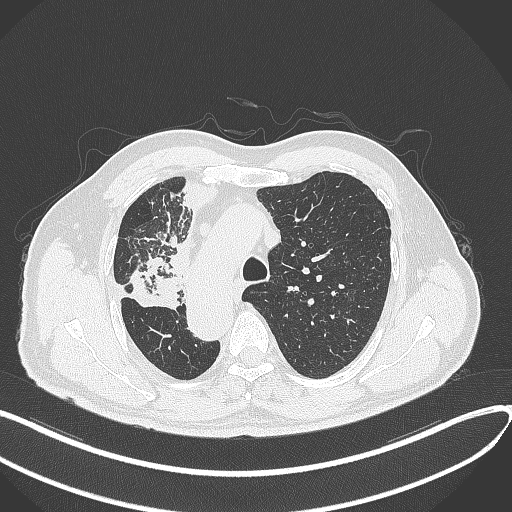
Chest CT, one axial slice. Slice 233 of 300 in the series (ordered by position). Reconstruction kernel B70f. 120 kVp. Lung window (W 1500 / L -600 HU). 512 × 512 image matrix, field of view 400 × 400 mm. Male patient, age 67 years. Case-level facts recorded for this patient, not image findings: clinical TNM (as recorded): T2a N0 M0.
Structures marked on this image (rectangle marked by the reading radiologist):
- lung tumour (recorded histology: squamous cell carcinoma): box from (x=128, y=252) to (x=182, y=313) px